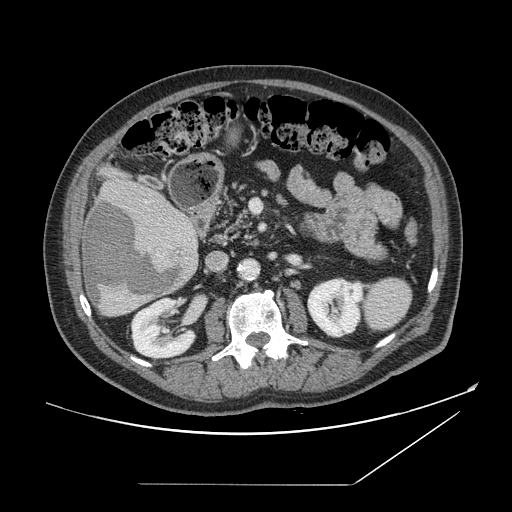
Contrast-enhanced abdominal CT, one axial slice. Position 69 of 166 along the scan axis. 120 kVp. Intravenous contrast given. Soft-tissue window (W 400 / L 40 HU). 512 × 512 image matrix, field of view 416 × 416 mm. Male patient, age 80 years. Case-level facts recorded for this patient, not image findings: diagnosis: colorectal cancer liver metastases, imaged before liver resection; multiple liver metastases: no; largest metastasis: 2.2 cm.
Annotated regions visible in this slice (manually delineated by an expert):
- liver: box from (x=81, y=178) to (x=199, y=317) px
- planned liver remnant (the part of the liver to remain after resection): (x=109, y=177)–(x=181, y=216)
- liver metastasis: (x=84, y=199)–(x=181, y=308)